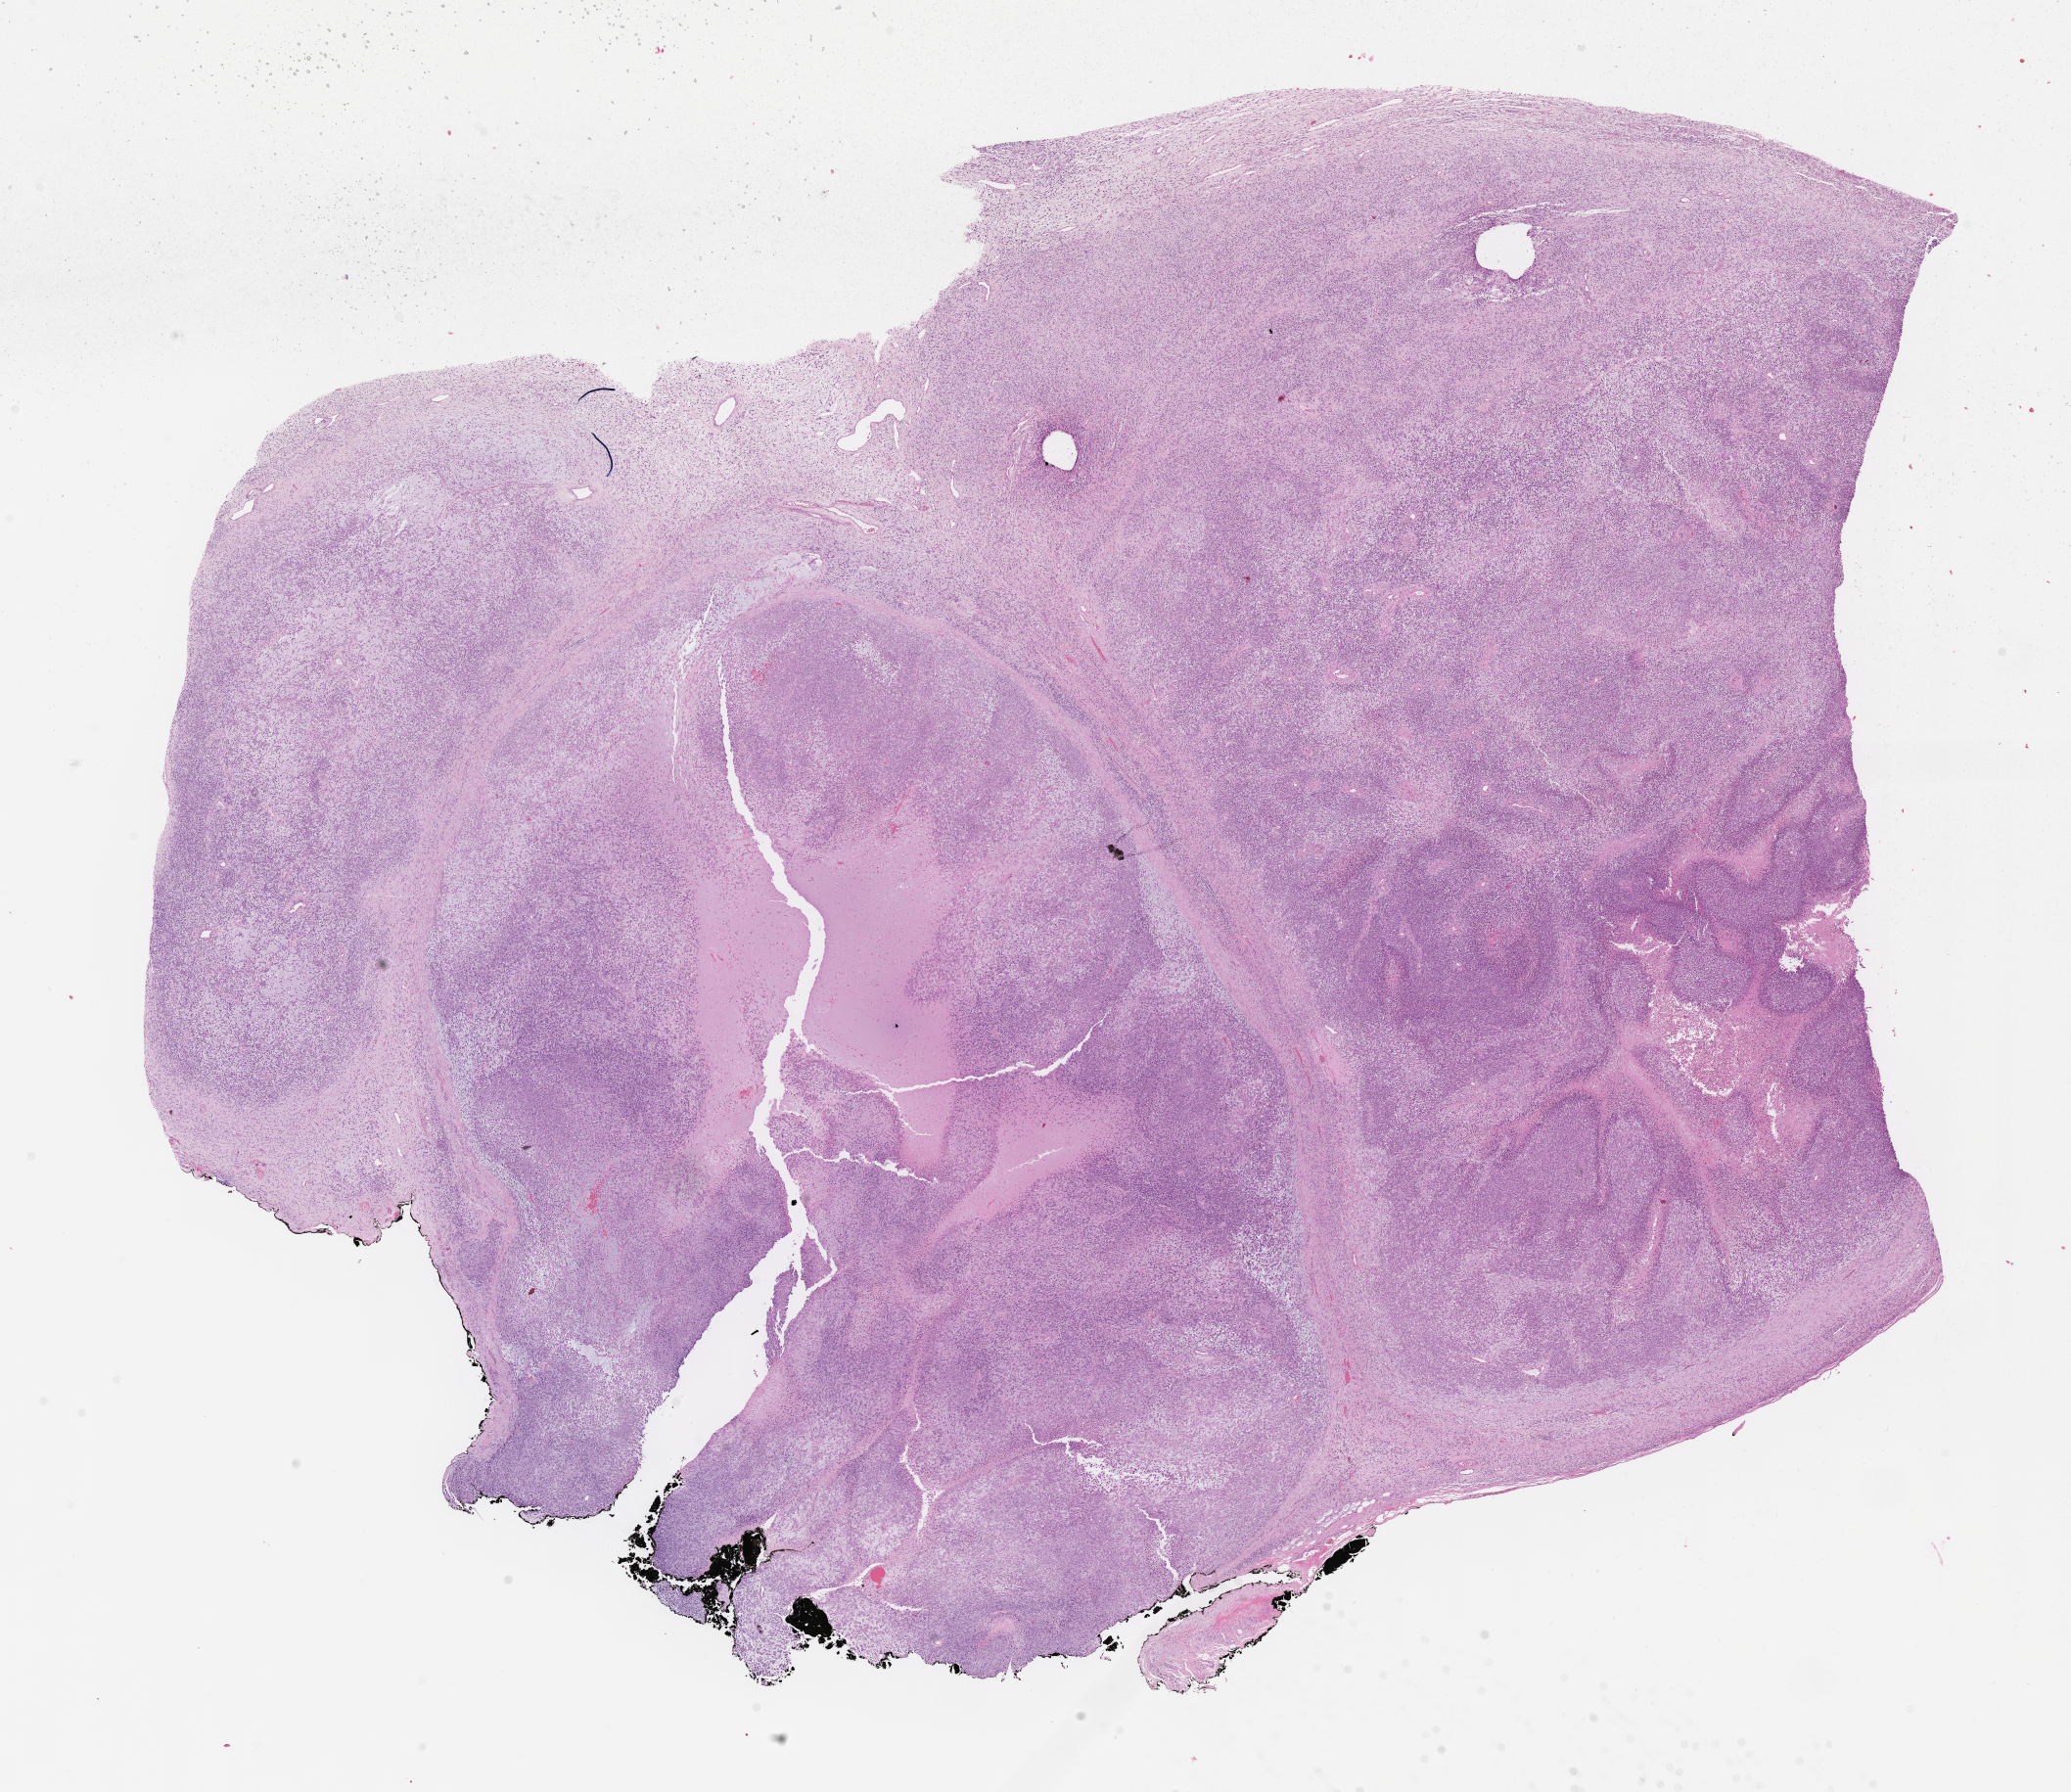
Whole-slide image, H&E stain of tumor tissue, a low-resolution overview of the entire scanned area, about 17.1 x 14.8 mm. Formalin-fixed, paraffin-embedded (FFPE) tissue. Site: paratesticular, left. Patient: male, age 1.6 years at diagnosis.
- primary site (case record): testis-Paratestis
- stage (as recorded): 1
- diagnosis: rhabdomyosarcoma; histological classification: embryonal rhabdomyosarcoma